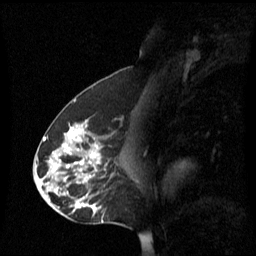
Breast MRI (dynamic contrast-enhanced), one sagittal slice; position 32 of 60 along the scan axis; dynamic contrast-enhanced series, image 2 of 3 at this slice position (ordered by acquisition); 1.5 T; TE 4.2 ms, TR 8.4 ms; 2.2 mm slice thickness; 256 × 256 image matrix, field of view 240 × 240 mm. Patient: female, 45 years. From the clinical record (not read from this slice): setting: breast cancer imaged before/during neoadjuvant chemotherapy; receptor status: HR-positive, HER2-negative.
Structures marked on this image (semi-automatically segmented with operator editing):
- analysis volume of interest (the breast-tissue region the enhancement analysis was run in; not a lesion): bounding box (x1, y1, x2, y2) in pixels: (38, 120, 131, 221)
- tumour enhancement mask (voxels above the 70 % enhancement threshold inside the analysis volume of interest): (52, 124, 101, 209)